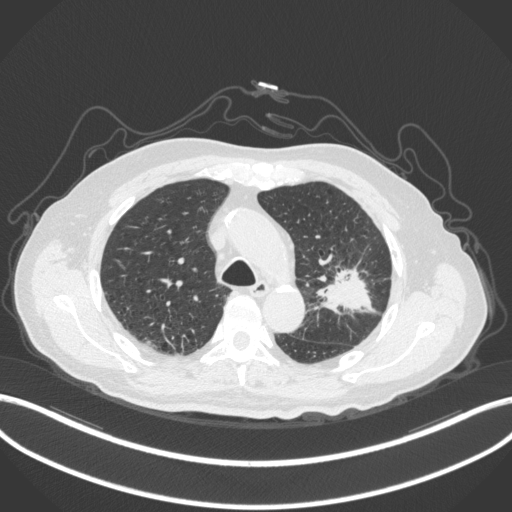
Chest CT, one axial slice; slice 207 of 331 in the series (ordered by position); 120 kVp; lung window (W 1500 / L -600 HU); 512 × 512 image matrix, field of view 400 × 400 mm. Patient: male, 79 years. Case-level facts recorded for this patient, not image findings: clinical TNM (as recorded): T2a N1 M1; histopathological grade: G3.
Outlined on this slice (rectangle marked by the reading radiologist):
- lung tumour (recorded histology: adenocarcinoma): bounding box <315,260,379,316> (left, top, right, bottom; pixels)